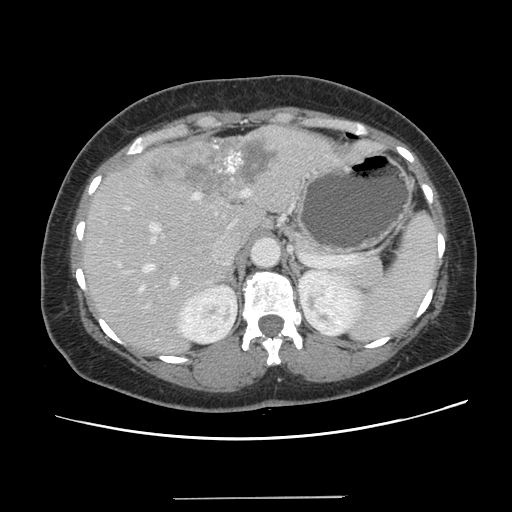
Contrast-enhanced abdominal CT, one axial slice. 120 kVp. Intravenous contrast given. Soft-tissue window (W 400 / L 40 HU). 512 × 512 image matrix. Female patient, age 53 years. From the clinical record (not read from this slice): diagnosis: colorectal cancer liver metastases, imaged before liver resection; multiple liver metastases: no; largest metastasis: 14.5 cm.
Outlined on this slice (expert manual segmentation):
- hepatic veins: bounding box [x1, y1, x2, y2] px = [139, 193, 199, 291]
- liver: [84, 127, 376, 354]
- planned liver remnant (the part of the liver to remain after resection): [84, 208, 263, 354]
- portal vein (with intrahepatic branches): [150, 190, 248, 289]
- liver metastasis: [148, 139, 275, 195]